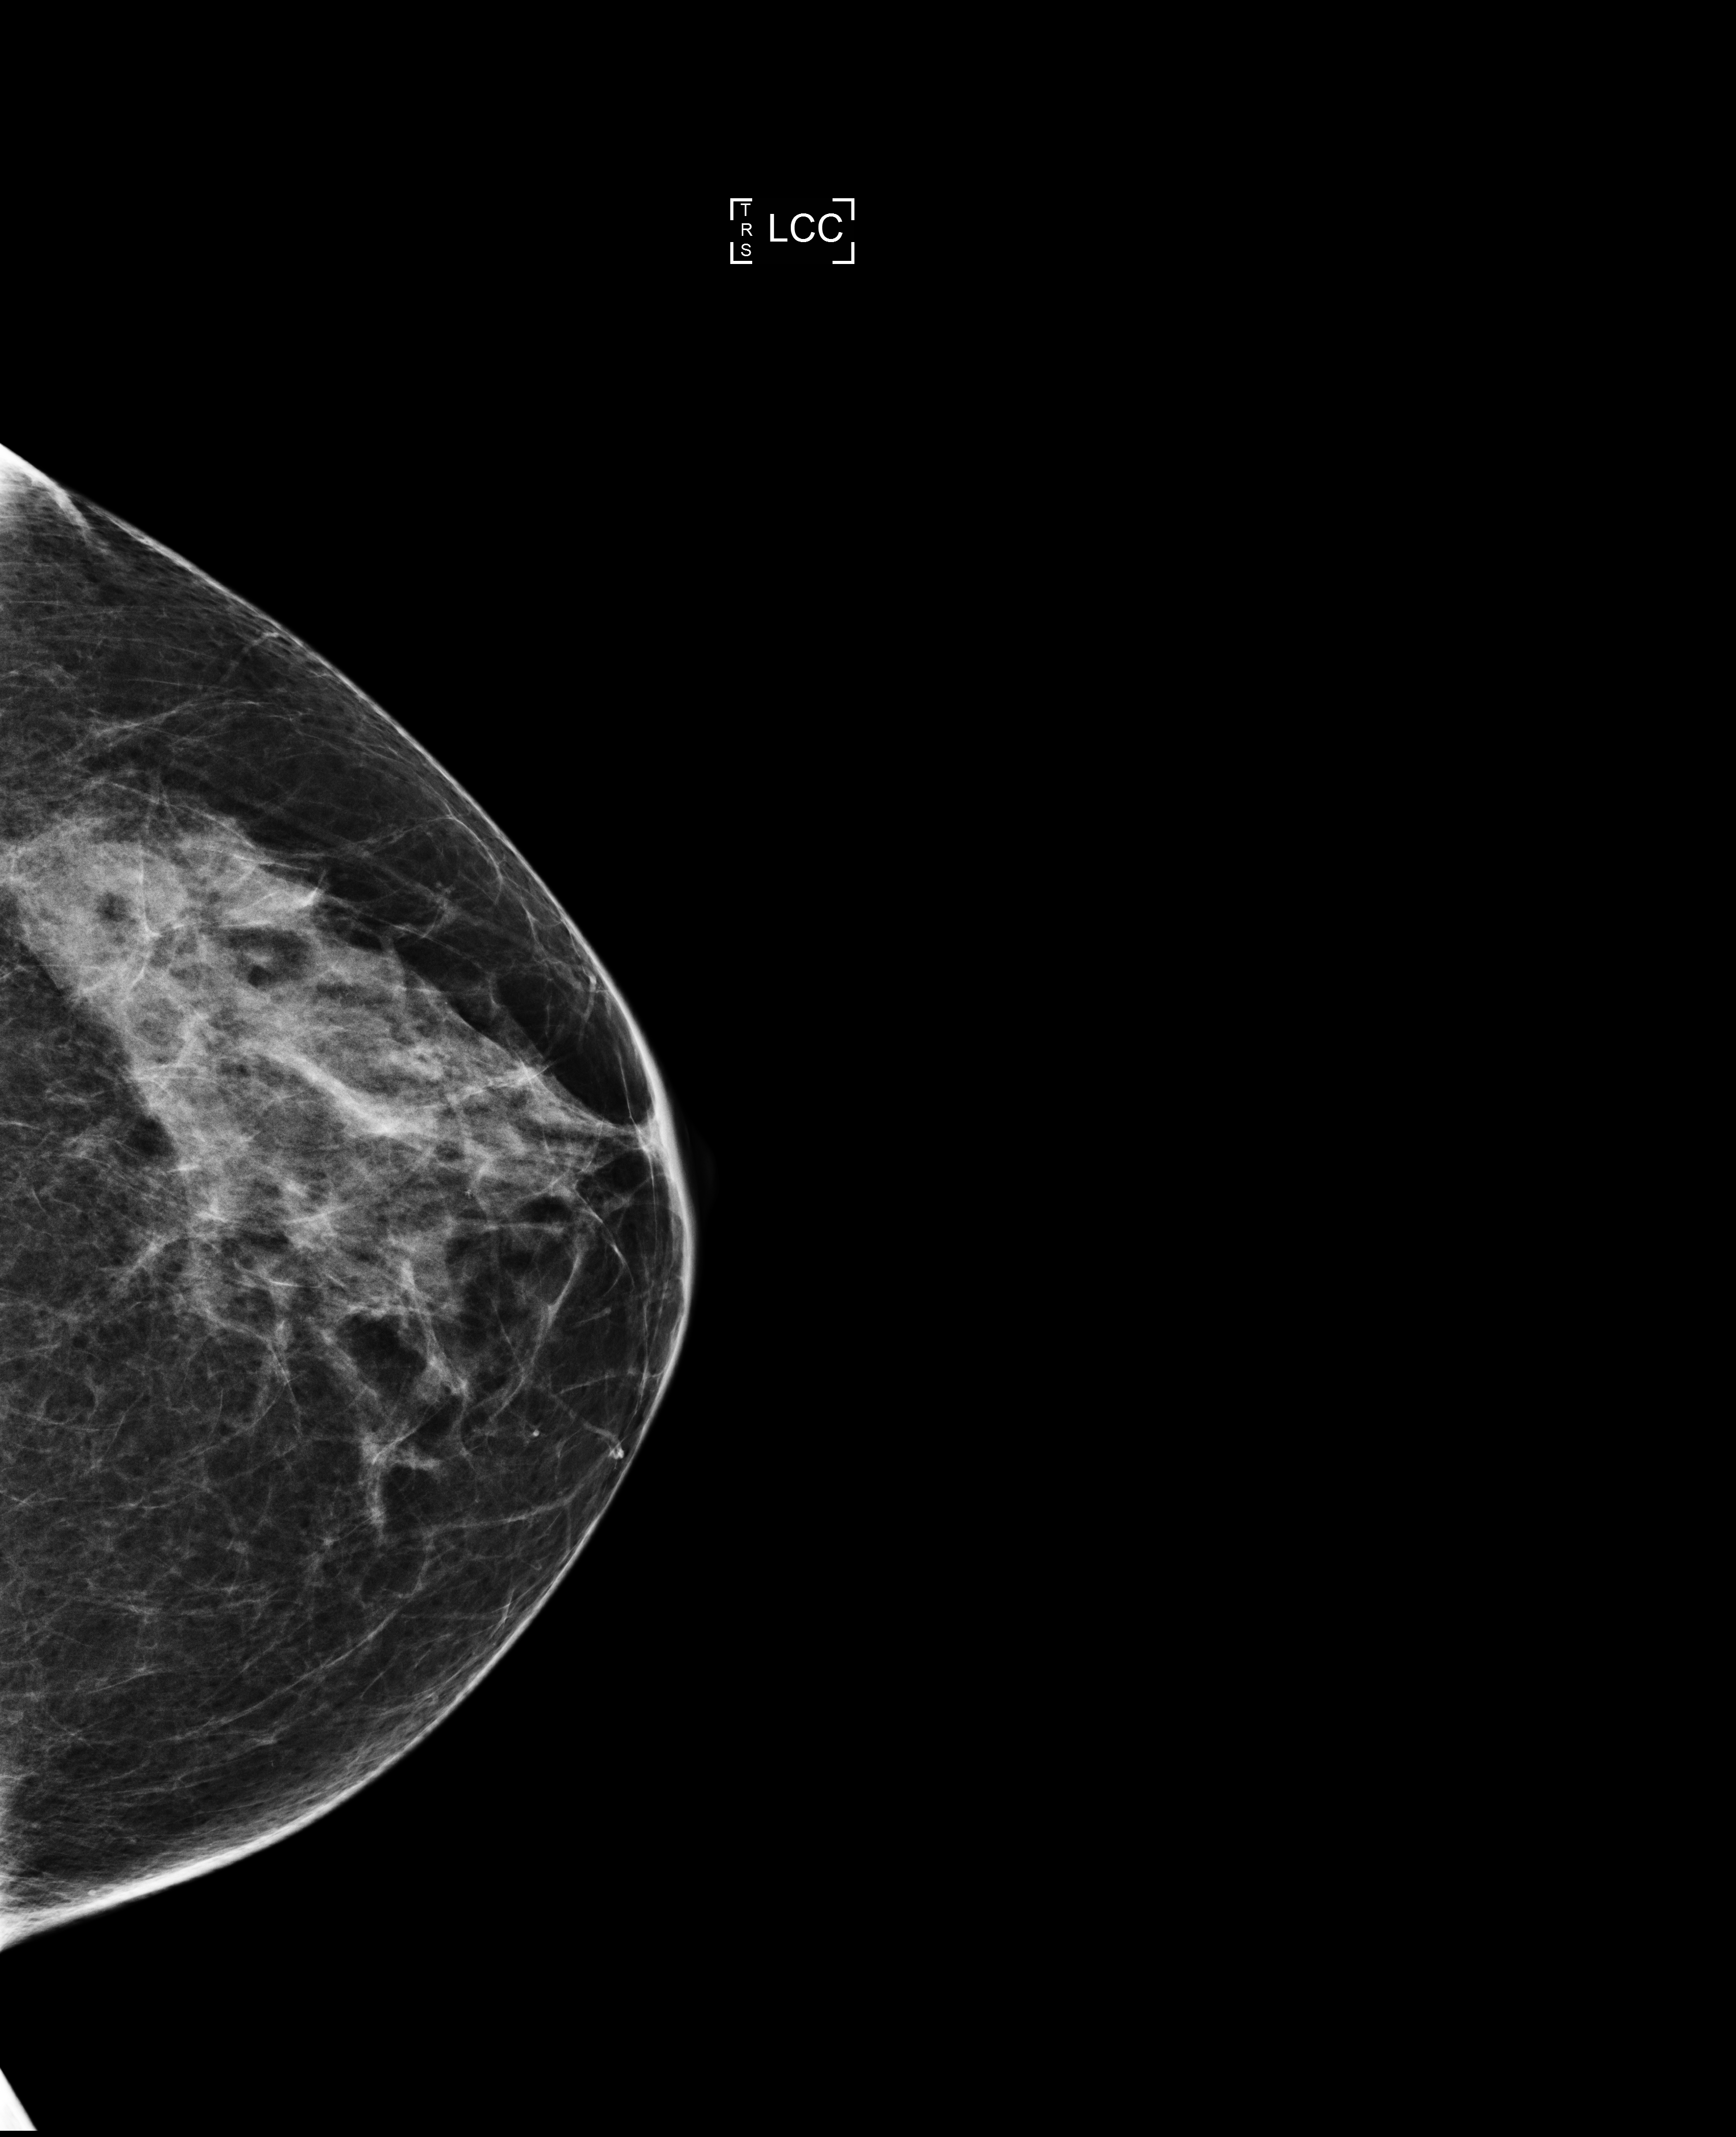
Annual screening mammography examination. Patient: female, 64 years.
Image type: full-field digital mammogram. Breast: left. Projection: craniocaudal (CC) view.